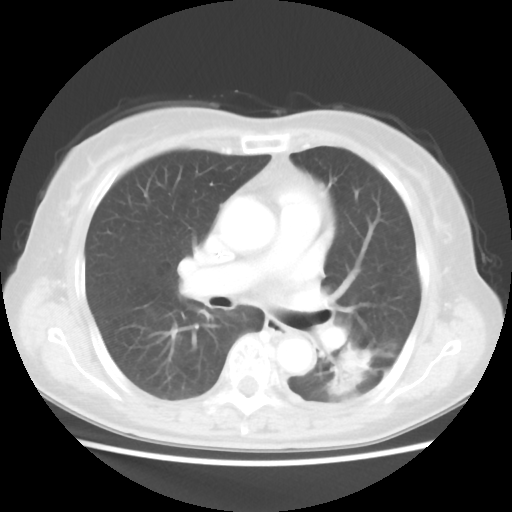
Chest CT, one axial slice; 100 kVp; lung window (W 1500 / L -600 HU); 512 × 512 image matrix. Female patient, age 69 years. From the clinical record (not read from this slice): clinical TNM (as recorded): T1c N0 M0.
Structures marked on this image (rectangle marked by the reading radiologist):
- lung tumour (recorded histology: adenocarcinoma): box from (x=333, y=340) to (x=372, y=400) px